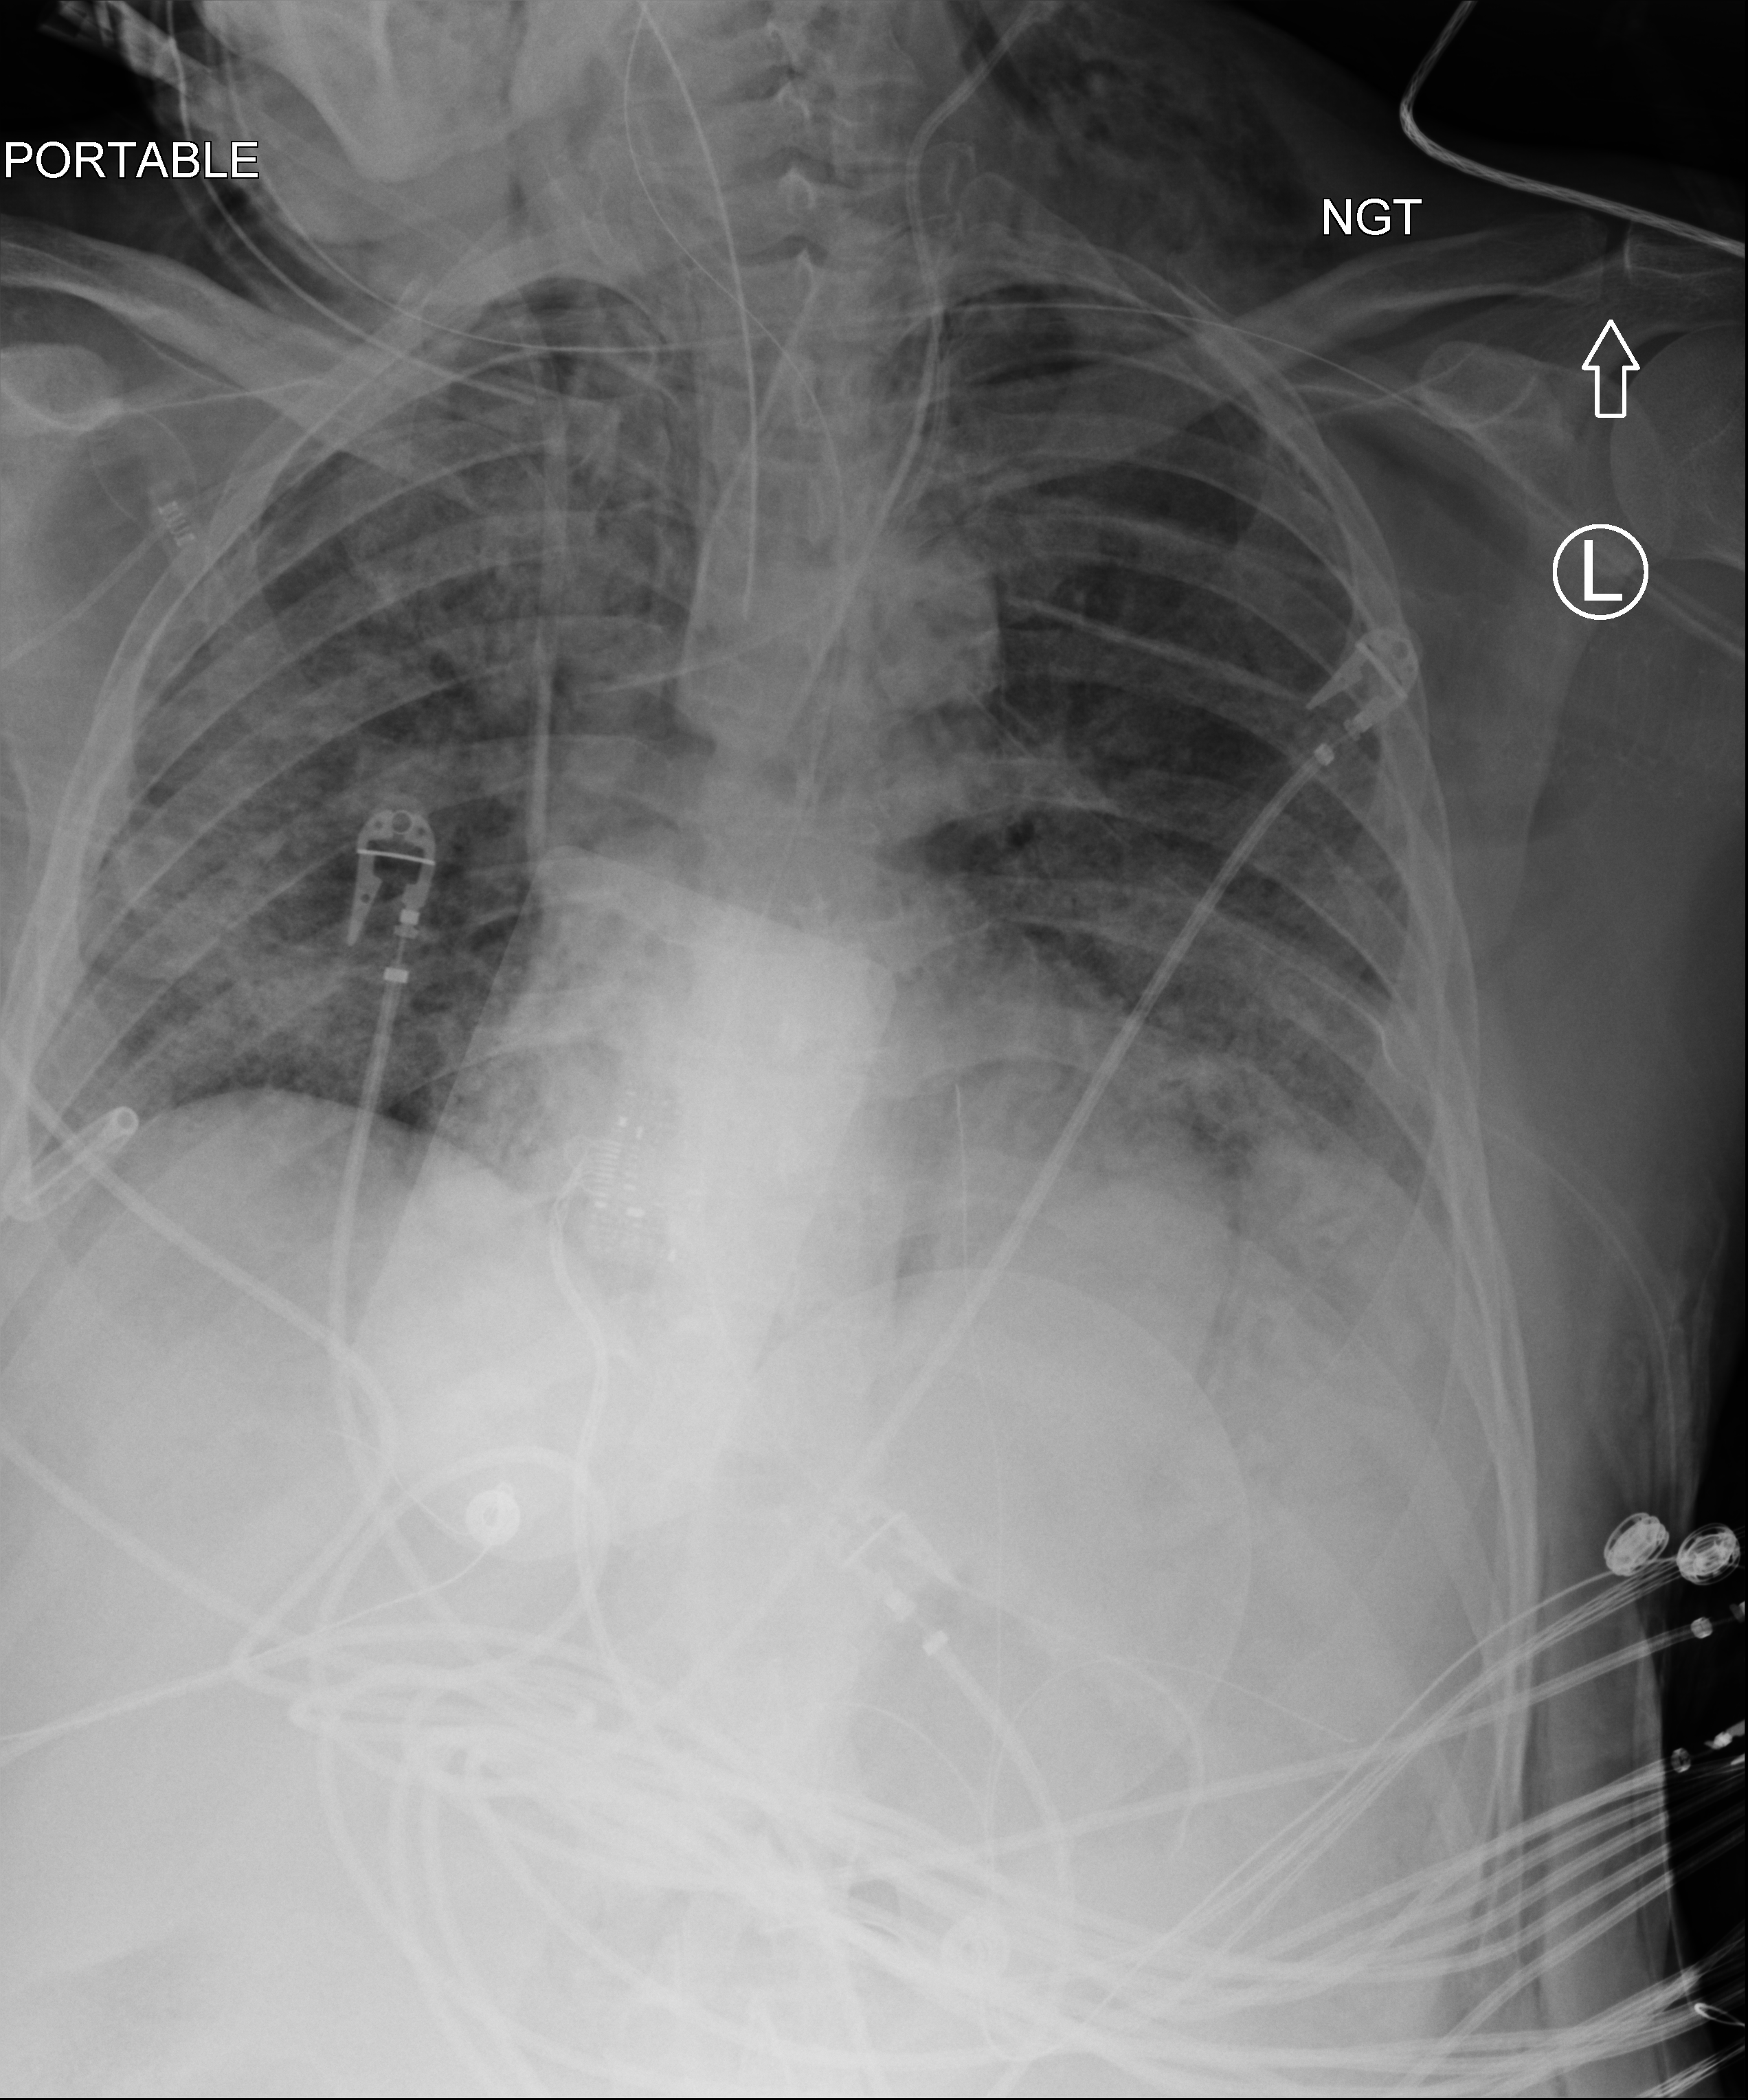
Chest X-ray (portable); anteroposterior (AP) projection. Patient hospitalised with COVID-19; male, aged 18–59 years.
From the hospital-stay record, not from the radiograph (when in the stay this image was taken is not recorded): admitted to intensive care during this hospital stay: yes; COPD (admission record): no; chronic kidney disease (admission record): no.